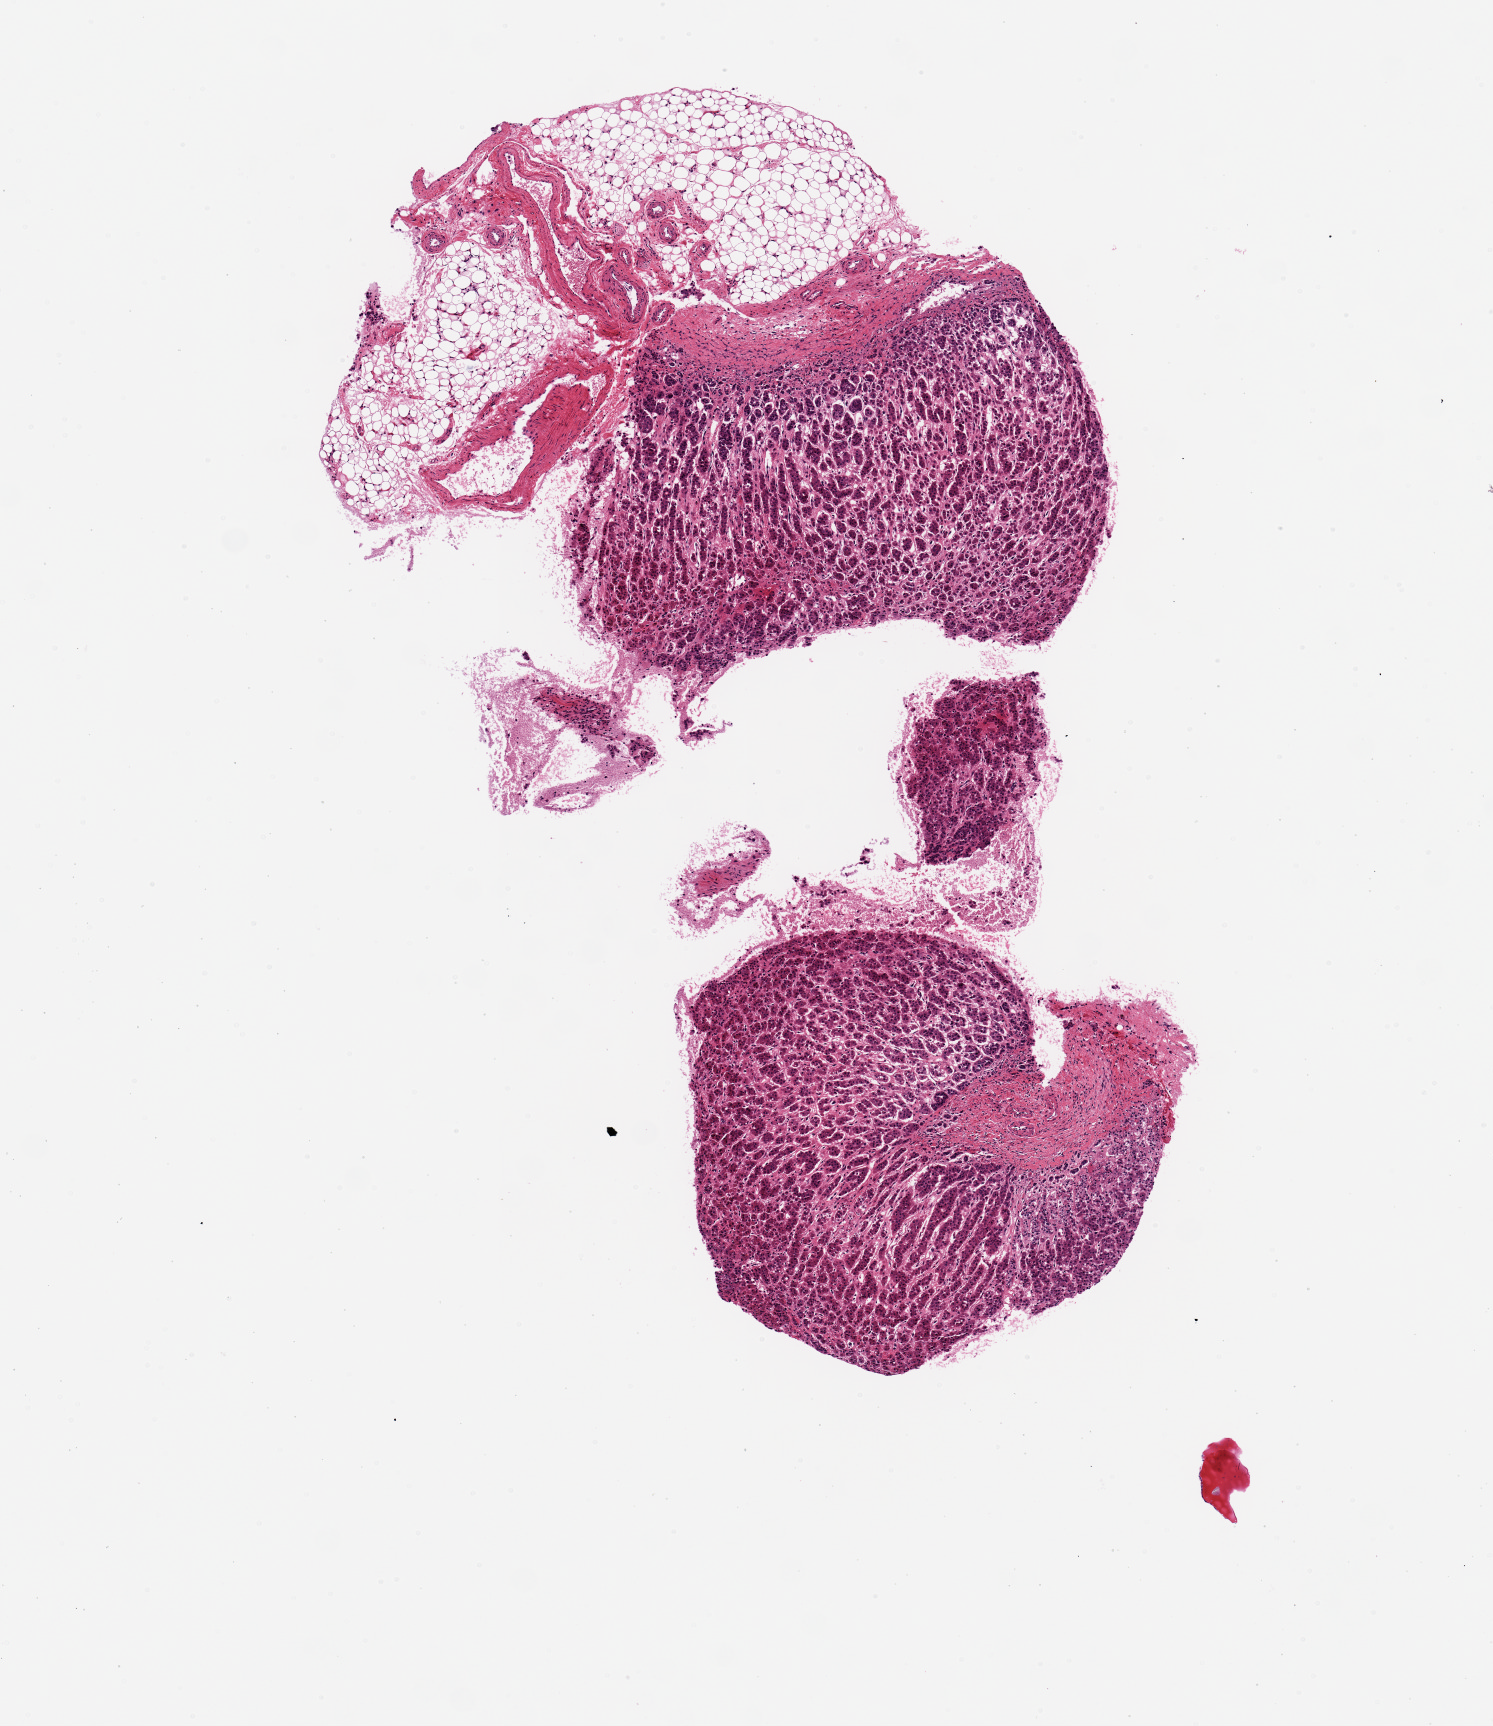
Whole-slide image, haematoxylin and eosin stain, brightfield, low-resolution overview of the scanned area, about 5.9 x 6.8 mm, PAXgene-fixed, paraffin-embedded tissue, sampled site (target tissue): adrenal gland, tissue donor sample. Female donor.
* reviewer comment on this tissue sample: 25% adipose